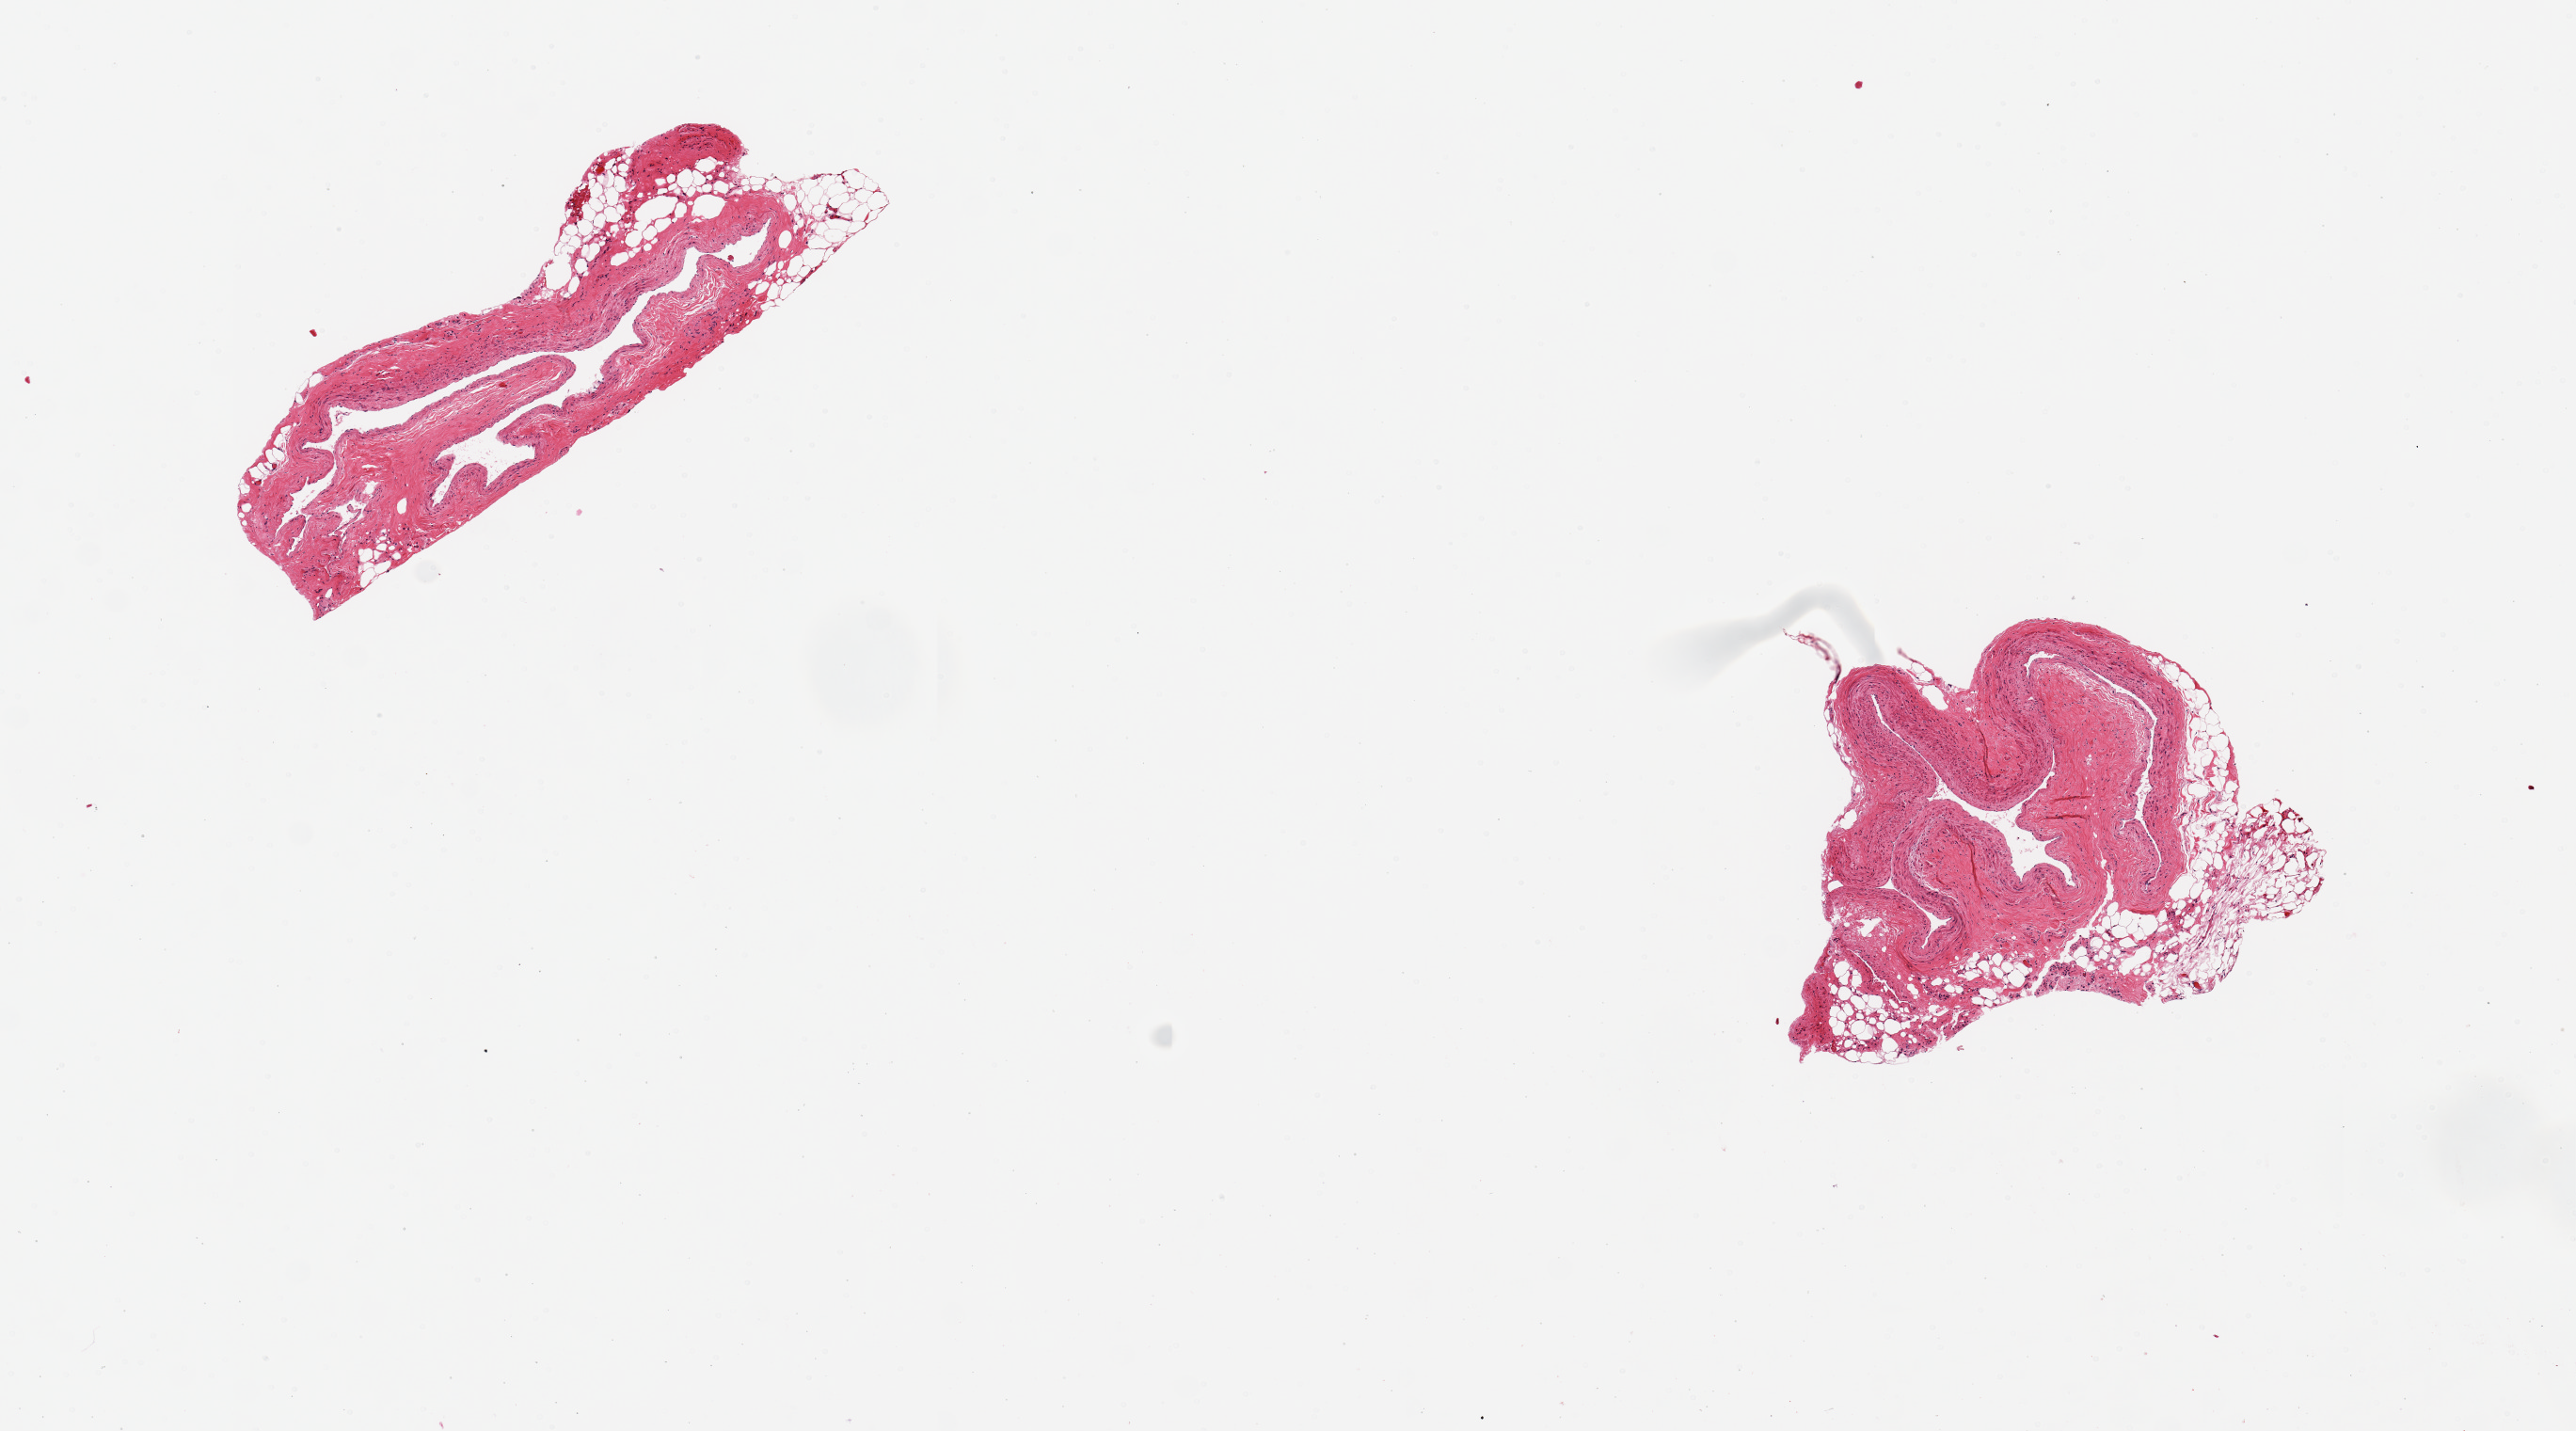
Digitized hematoxylin and eosin (H&E)-stained section — whole scanned area (about 10.8 x 6.0 mm) shown as a low-resolution overview, PAXgene-fixed paraffin-embedded (PFPE) section, target tissue: coronary artery, tissue donor sample.
- reviewer comment on this tissue sample: 2 pieces ~1.5mm d; Discontinuou adherent fat up to ~0.5mm